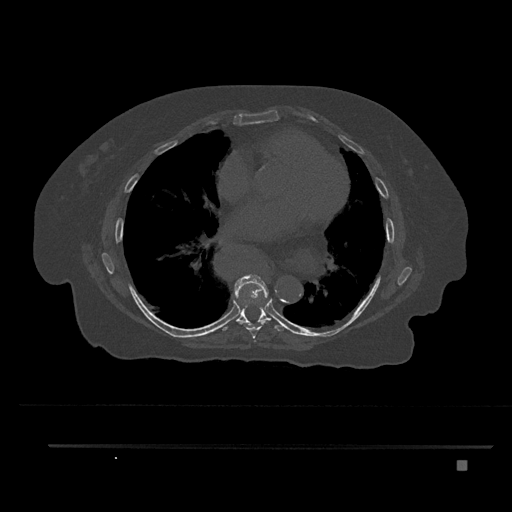
CT including the spine, one axial slice. Slice 464 of 797 in the series (ordered by position). Reconstruction kernel Br40s/3. Bone window (W 1800 / L 400 HU). 512 × 512 image matrix, field of view 437 × 437 mm. Female patient, age 76 years. Case-level facts recorded for this patient, not image findings: primary cancer: lung; vertebrae with lytic lesions (as recorded): T11, L3.
Outlined on this slice (semi-automatic segmentation, software-assisted and operator-edited):
- T6 vertebra: bounding box [x1, y1, x2, y2] px = [254, 340, 256, 342]
- T7 vertebra: [234, 274, 268, 339]
- T8 vertebra: [222, 303, 287, 332]